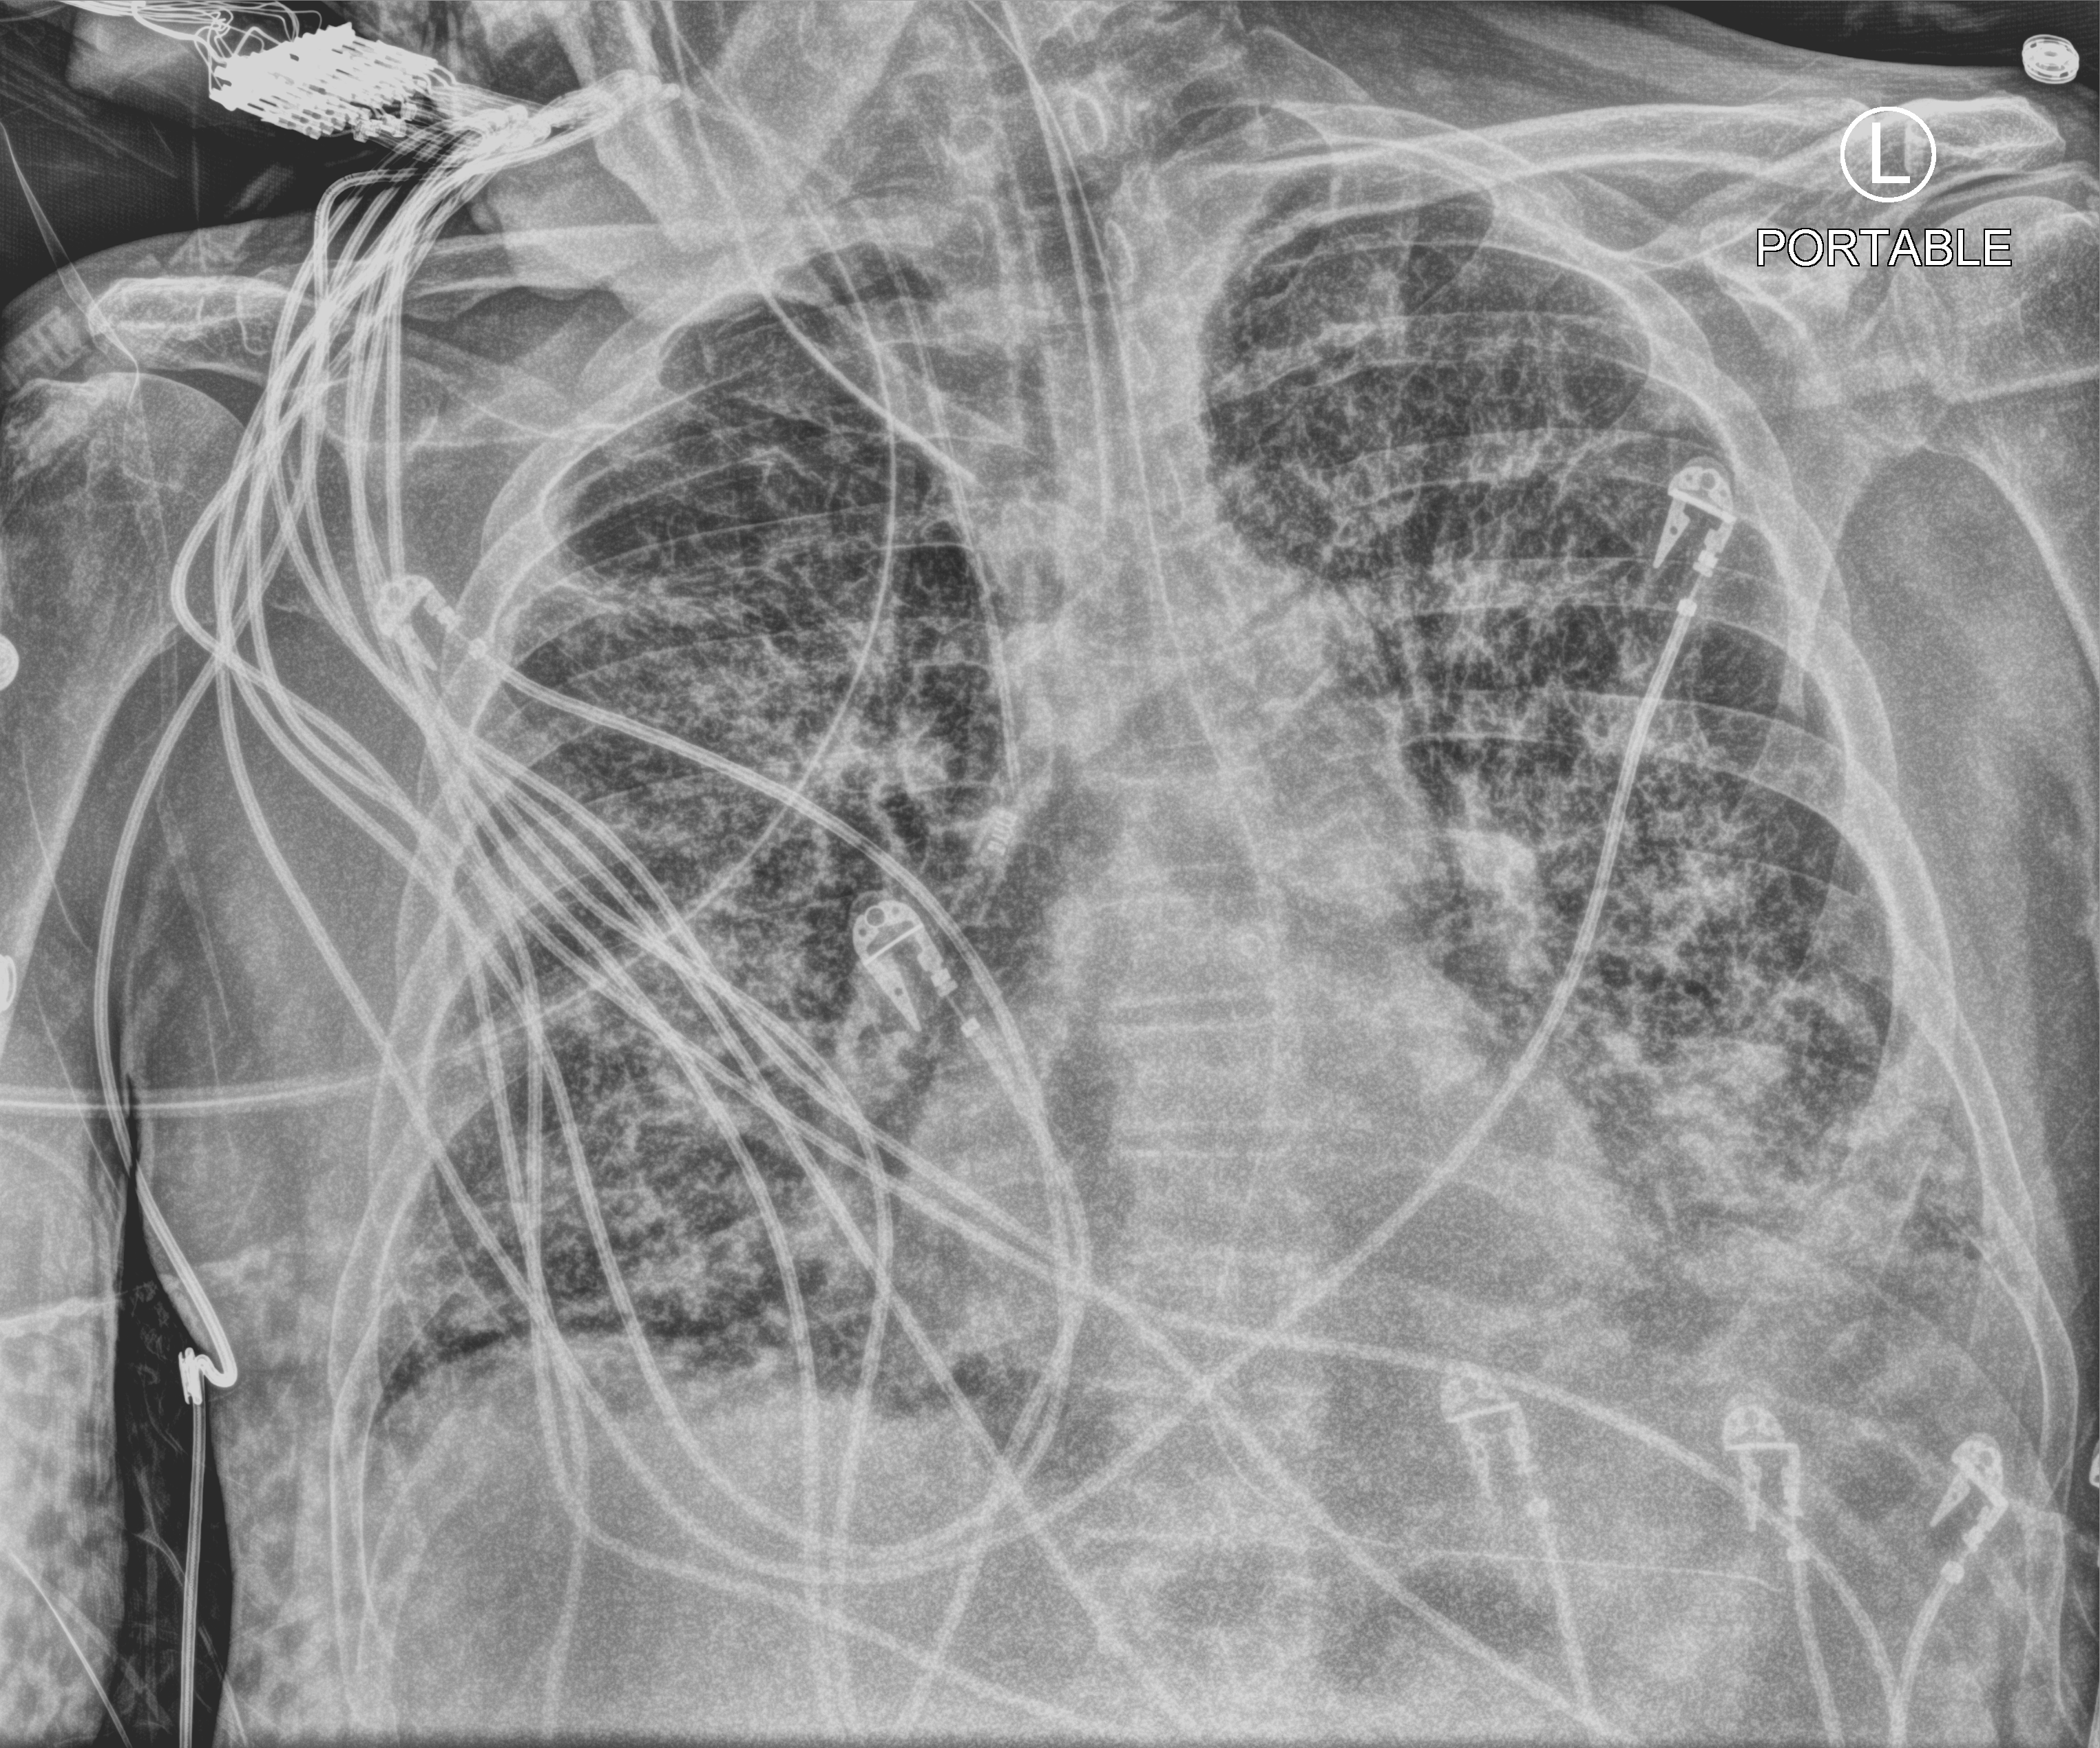
Portable chest radiograph; anteroposterior (AP) projection. Male patient hospitalised with COVID-19, age 75–90 years.
Admission-level facts for this patient (not findings on this image; timing relative to this image not recorded): admitted to intensive care during this hospital stay: yes.